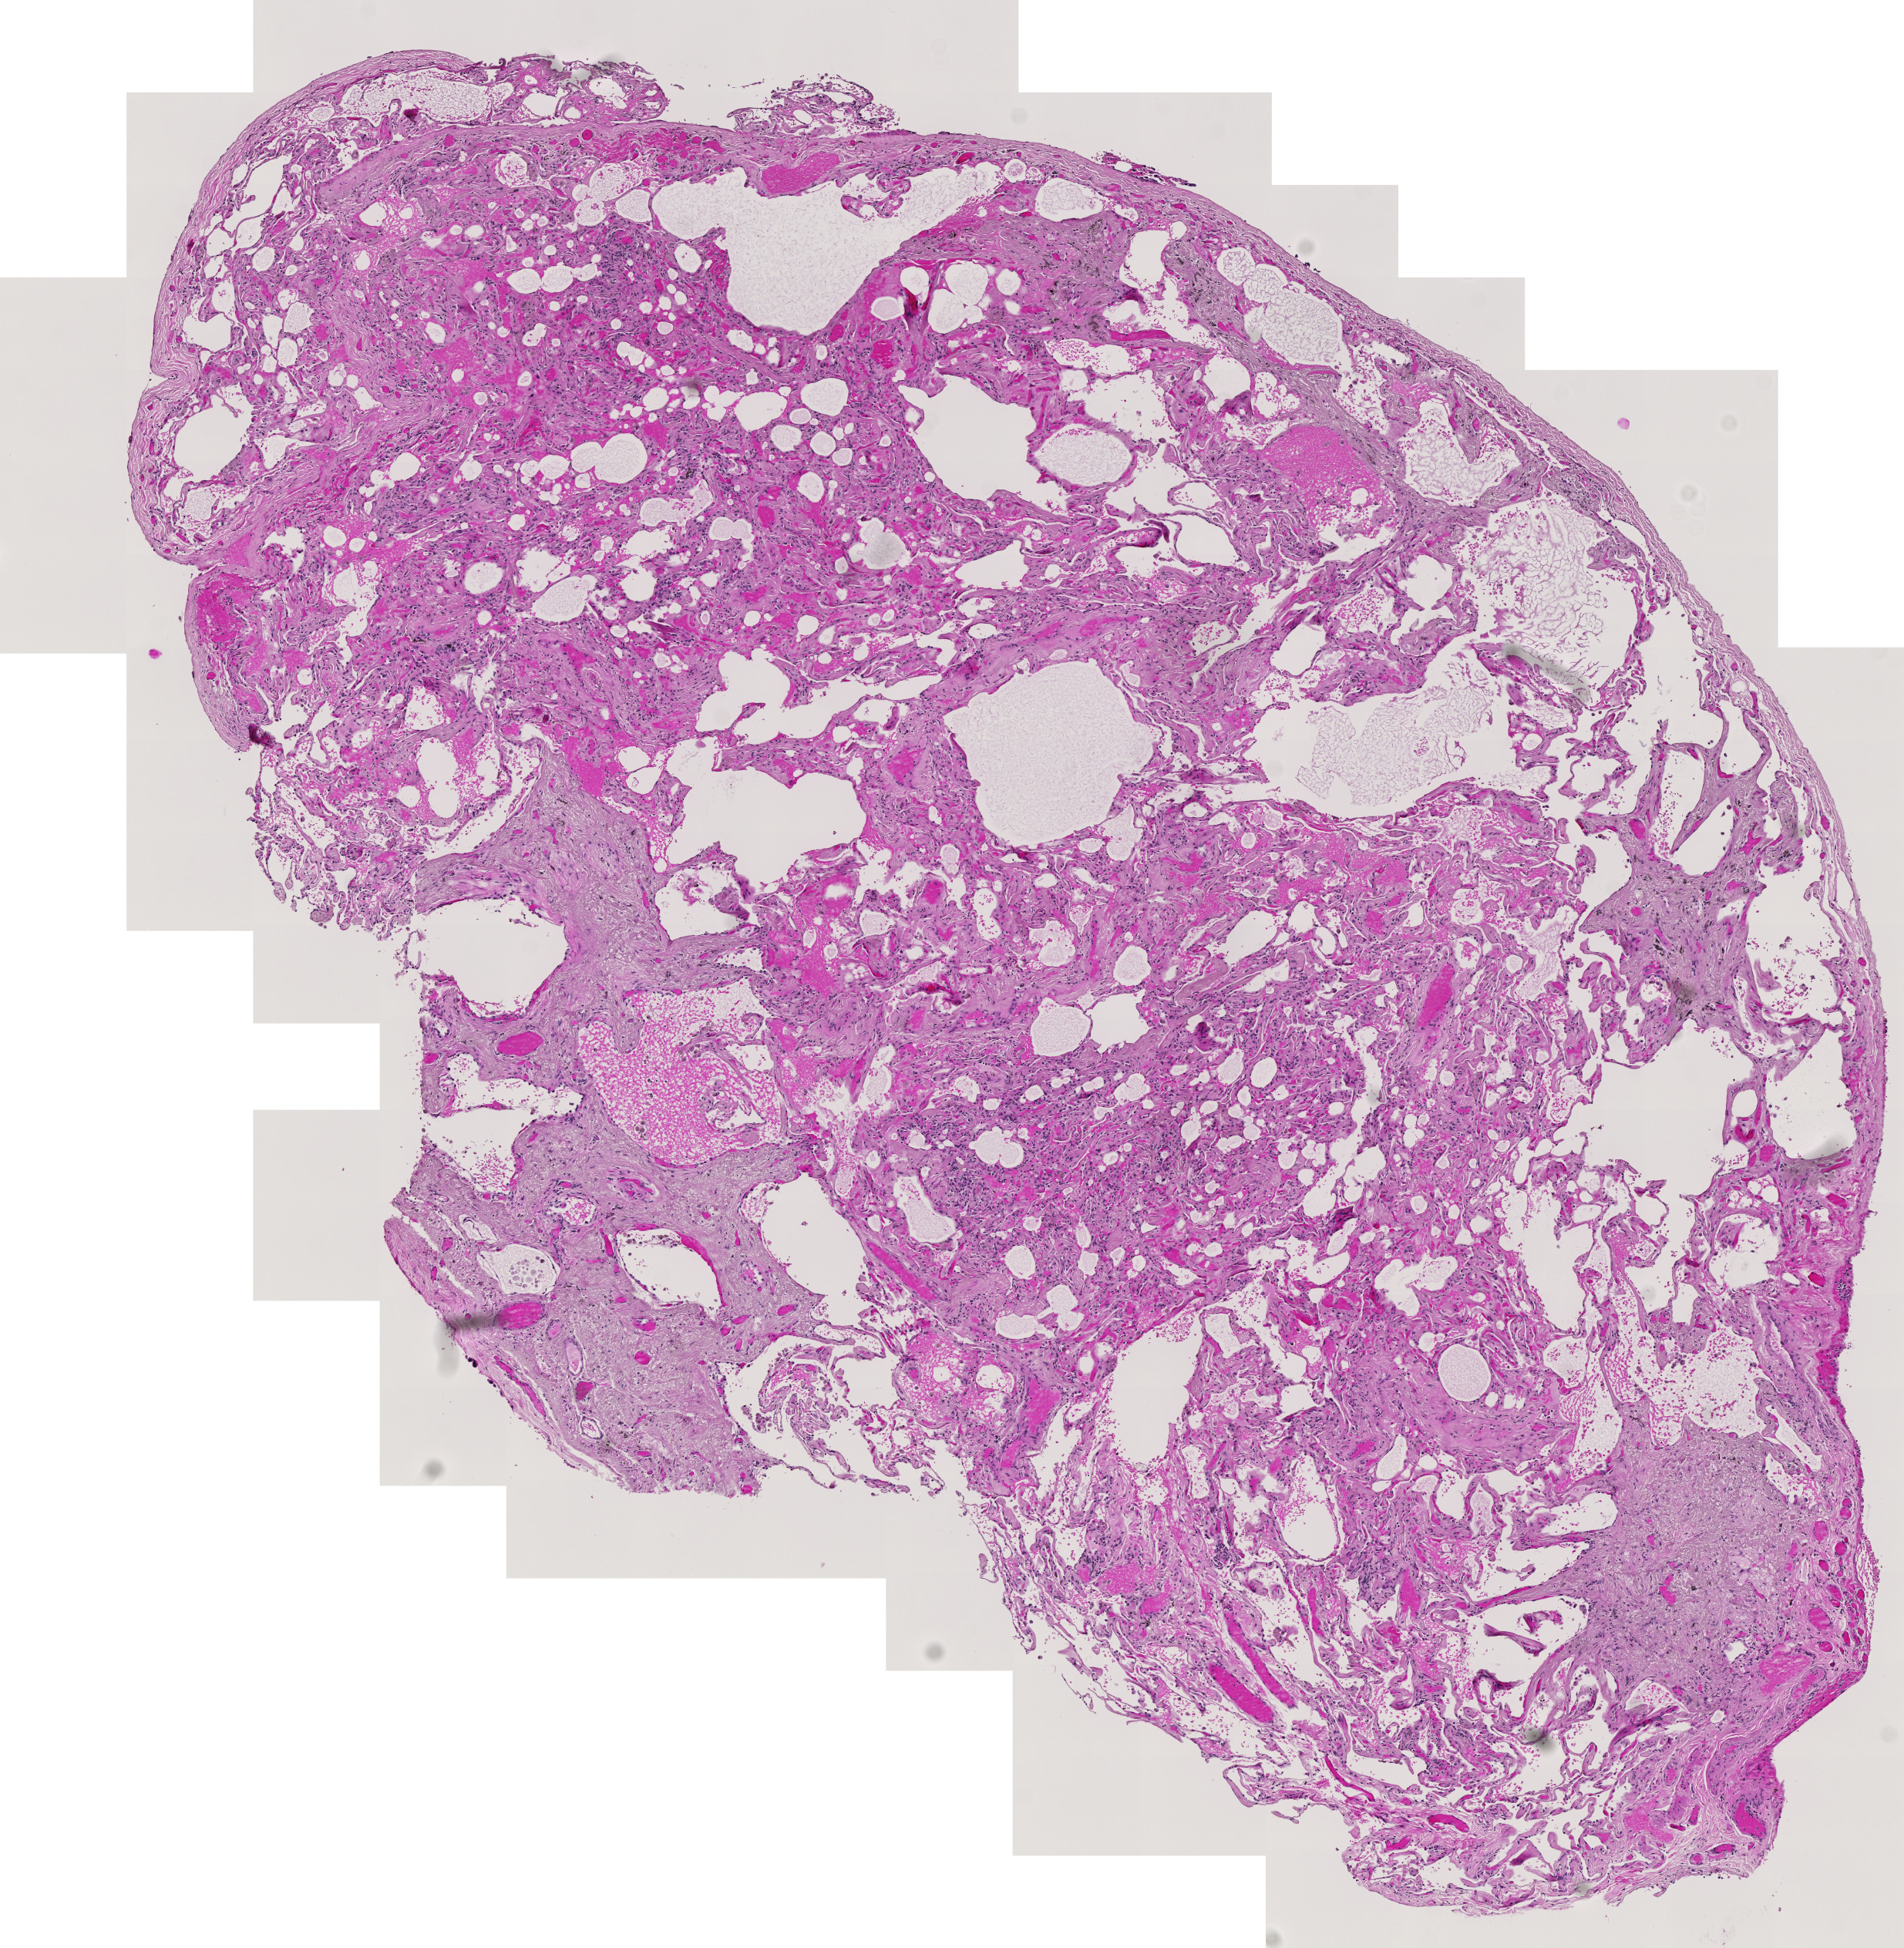
Digitized H&E tissue section (whole slide), whole scanned area (about 6.4 x 6.5 mm) shown as a low-resolution overview, normal (non-tumour) tissue sample, sampled site: lung. Female, 68 y/o.
This section: normal (non-tumour) tissue from the same patient. Patient diagnosis: Adenocarcinoma, NOS.